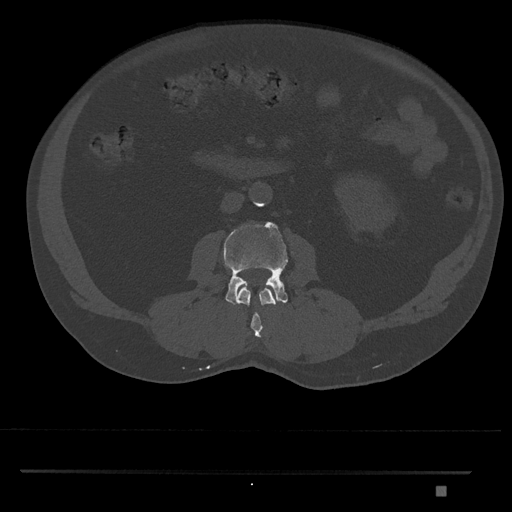
CT including the spine, one axial slice; slice 710 of 1134 in the series (ordered by position); reconstruction kernel Br40s/3; 120 kVp; bone window (W 1800 / L 400 HU); 512 × 512 image matrix, field of view 429 × 429 mm. Patient: male, 65 years. Case-level facts recorded for this patient, not image findings: primary cancer: prostate.
Outlined on this slice (semi-automatic segmentation, software-assisted and operator-edited):
- L2 vertebra: box from (x=238, y=286) to (x=276, y=338) px
- L3 vertebra: (x=223, y=221)–(x=288, y=305)